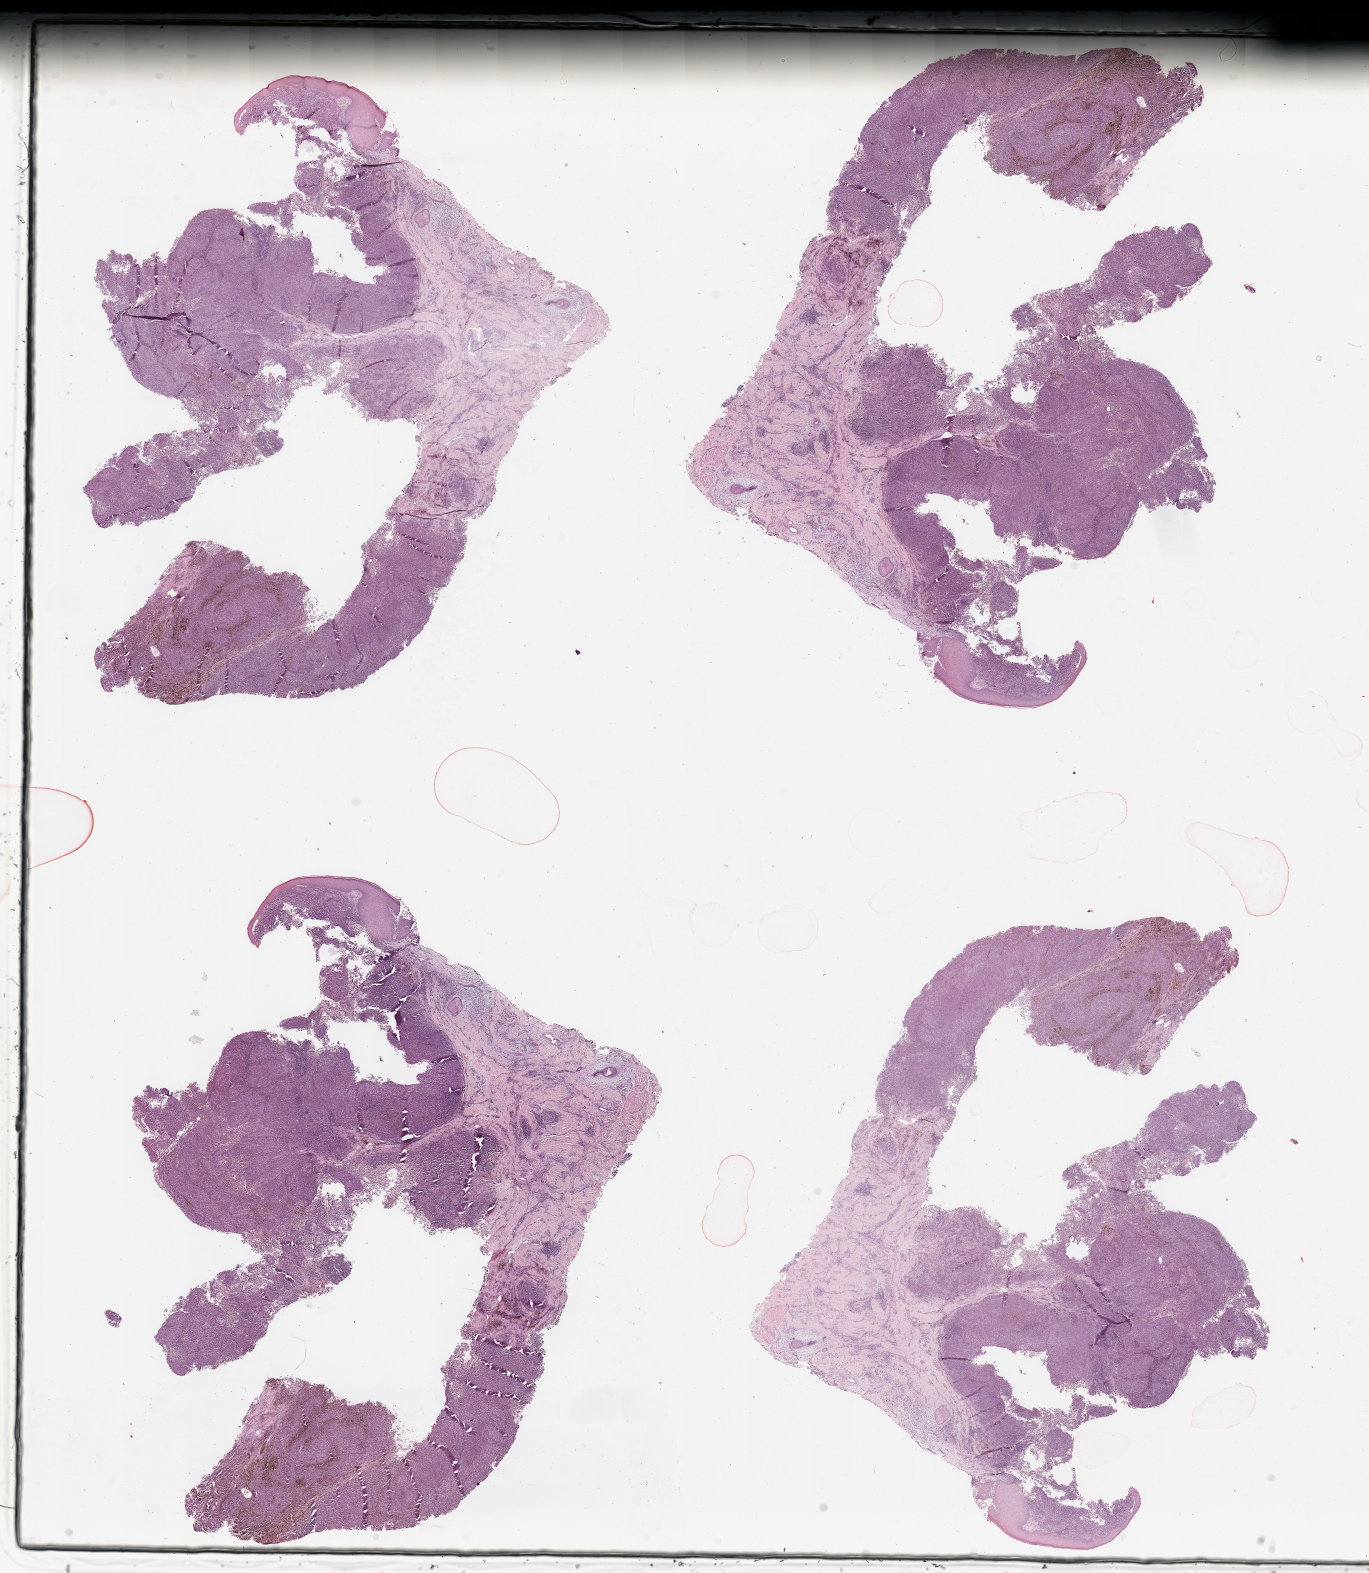
Digitized H&E-stained tissue section (whole slide) — whole scanned area (about 21.7 x 24.9 mm, slide scanned at 20x) shown as a low-resolution overview, melanoma tumour tissue; sampled site not recorded. Patient: male, age 60 years.
Primary tumour site (as recorded): trunk. Histologic diagnosis: Malignant melanoma, NOS.